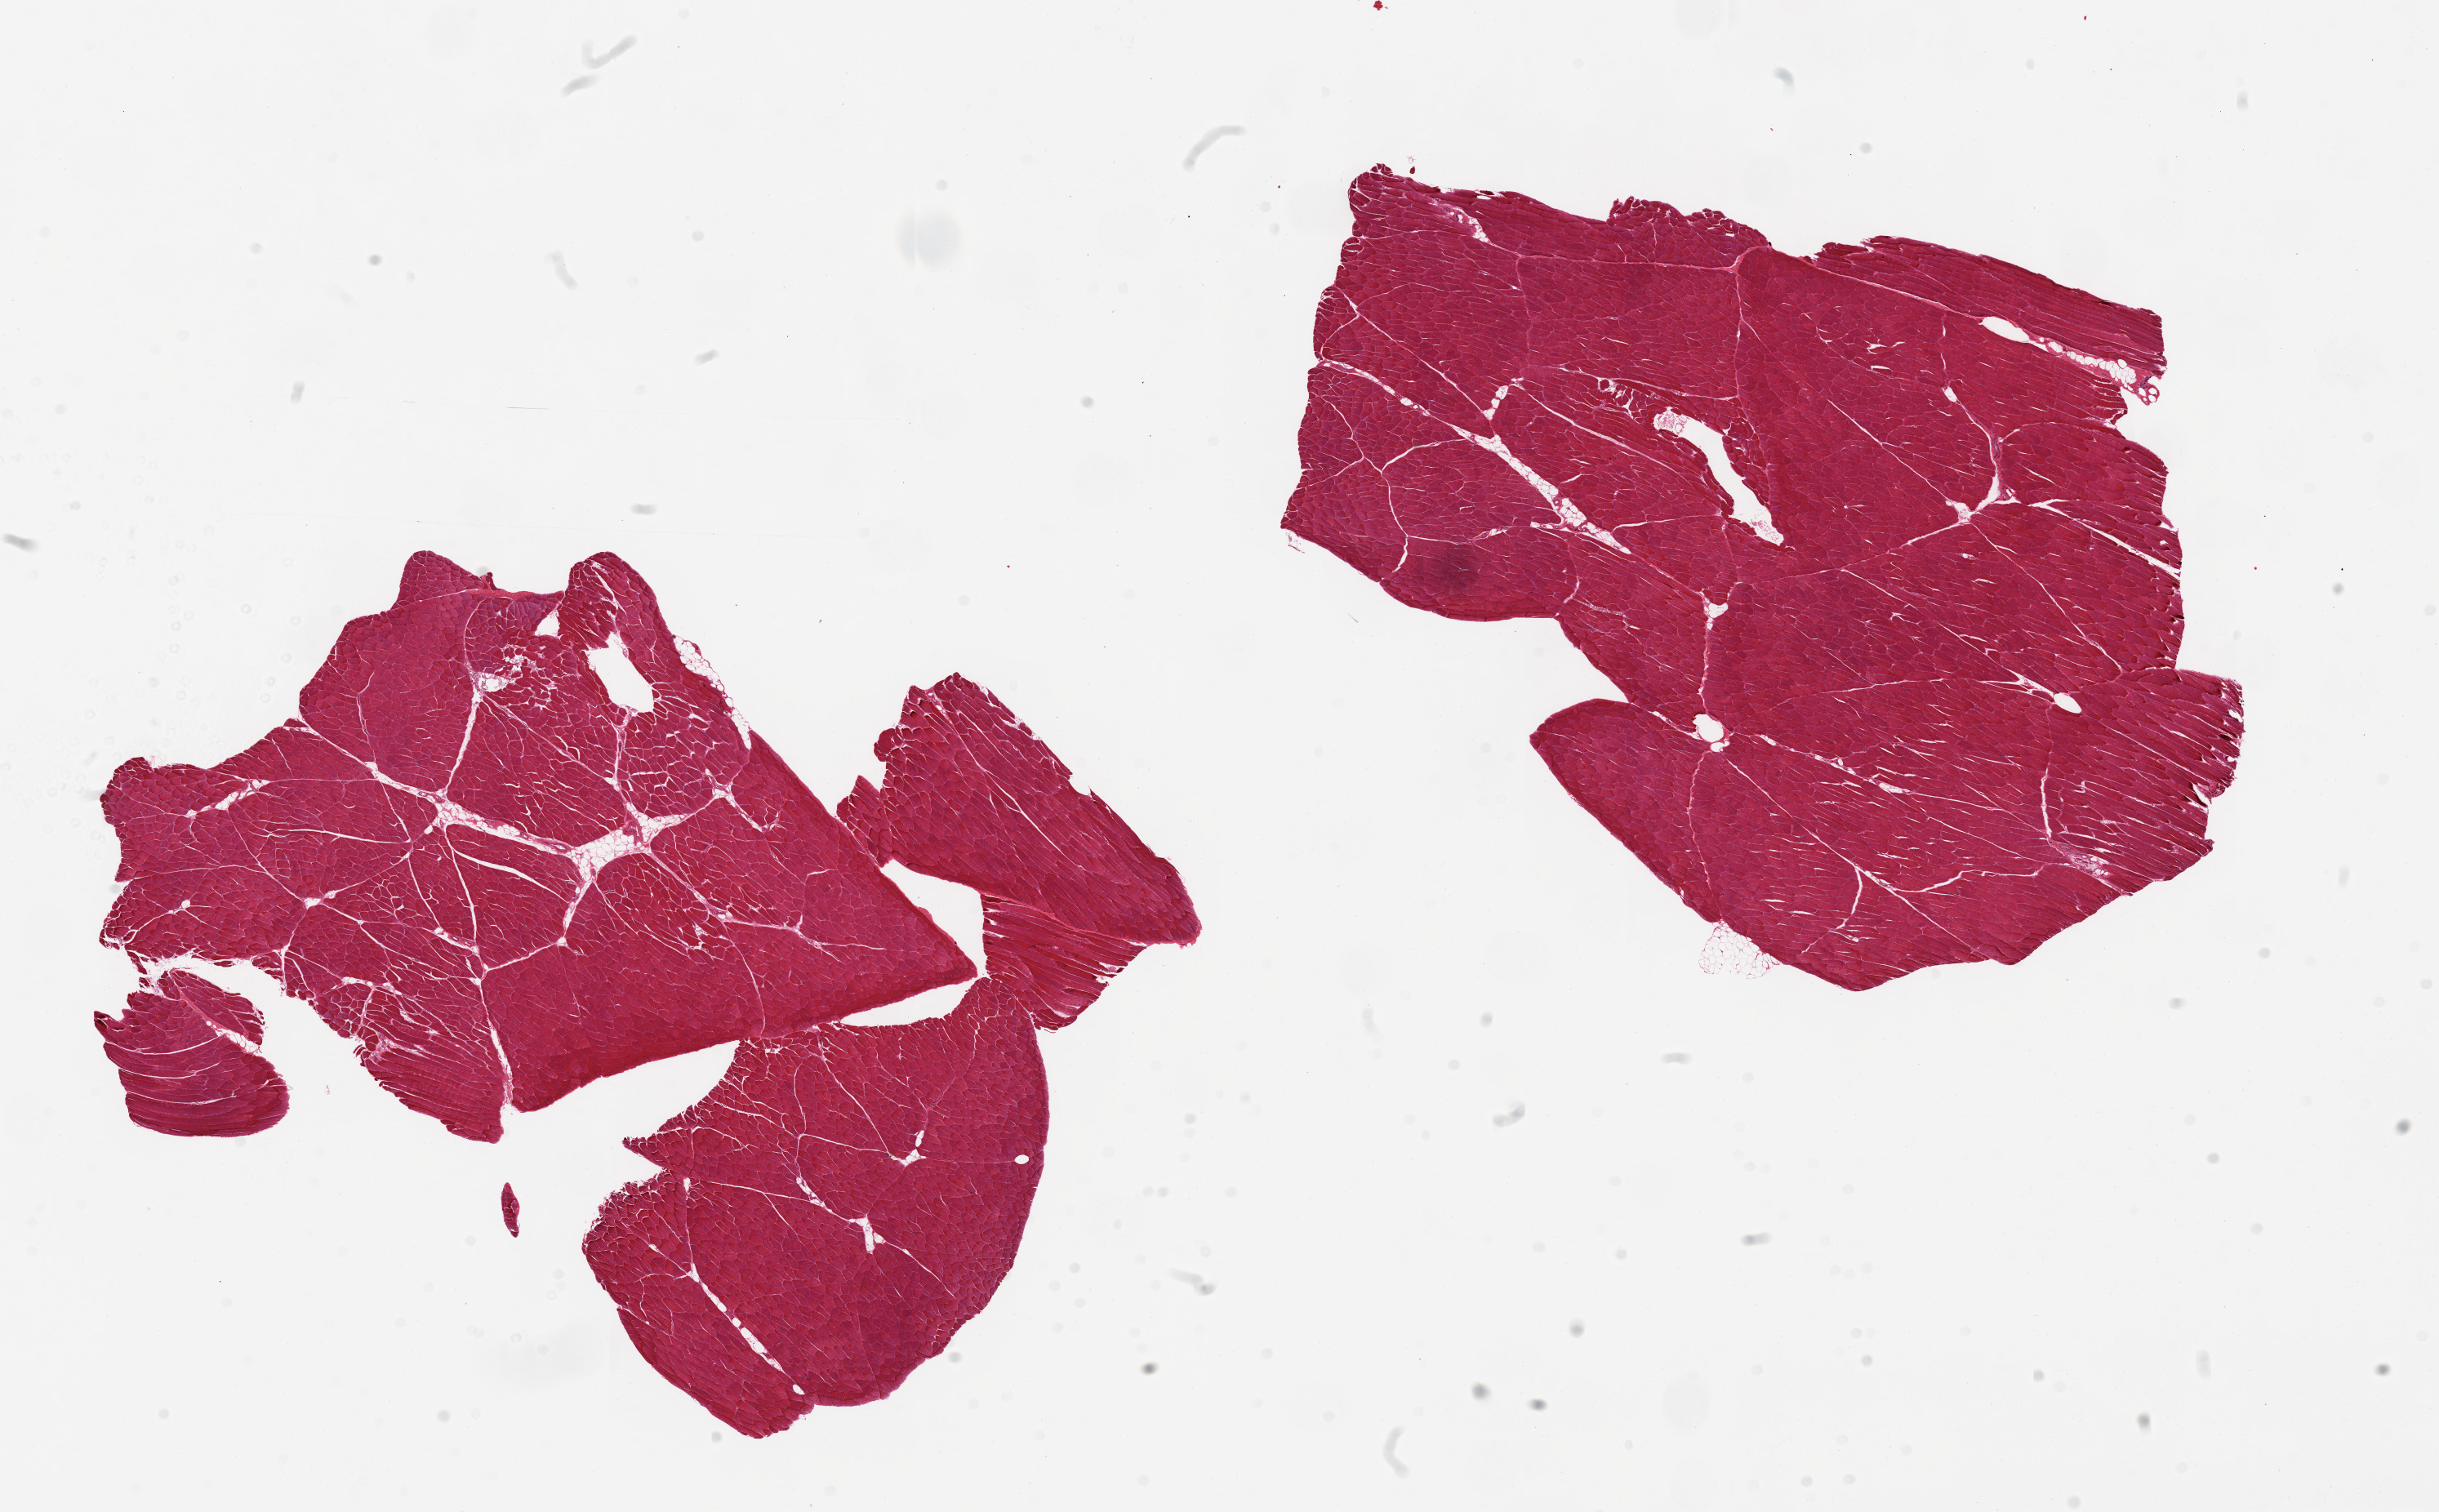
Whole-slide image, hematoxylin and eosin (H&E) stain, low-resolution overview of the scanned area, about 23.6 x 14.6 mm (from a 20x scan). PAXgene-fixed, paraffin-embedded tissue. Sampled site (target tissue): skeletal muscle. Tissue donor sample. Male donor.
Review note (as recorded): 2 pieces.